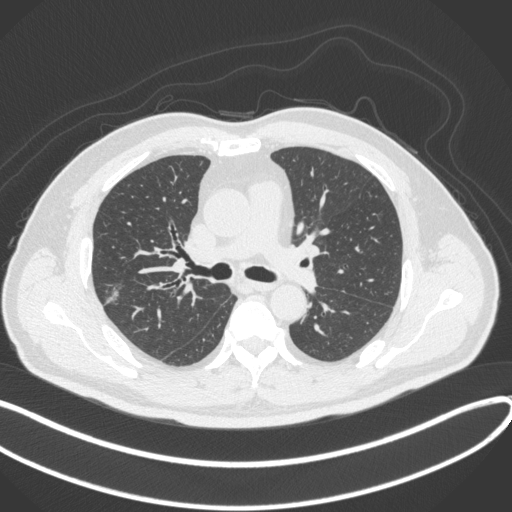
Chest CT, one axial slice. Position 210 of 373 along the scan axis. Reconstruction kernel B31f. 120 kVp. Lung window (W 1500 / L -600 HU). 1 mm slice thickness. 512 × 512 image matrix. Male patient, age 60 years. From the clinical record (not read from this slice): clinical TNM (as recorded): T1c N0 M0.
Annotated regions visible in this slice (bounding box drawn by a radiologist):
- lung tumour (recorded histology: adenocarcinoma): bounding box [x1, y1, x2, y2] px = [101, 278, 126, 311]